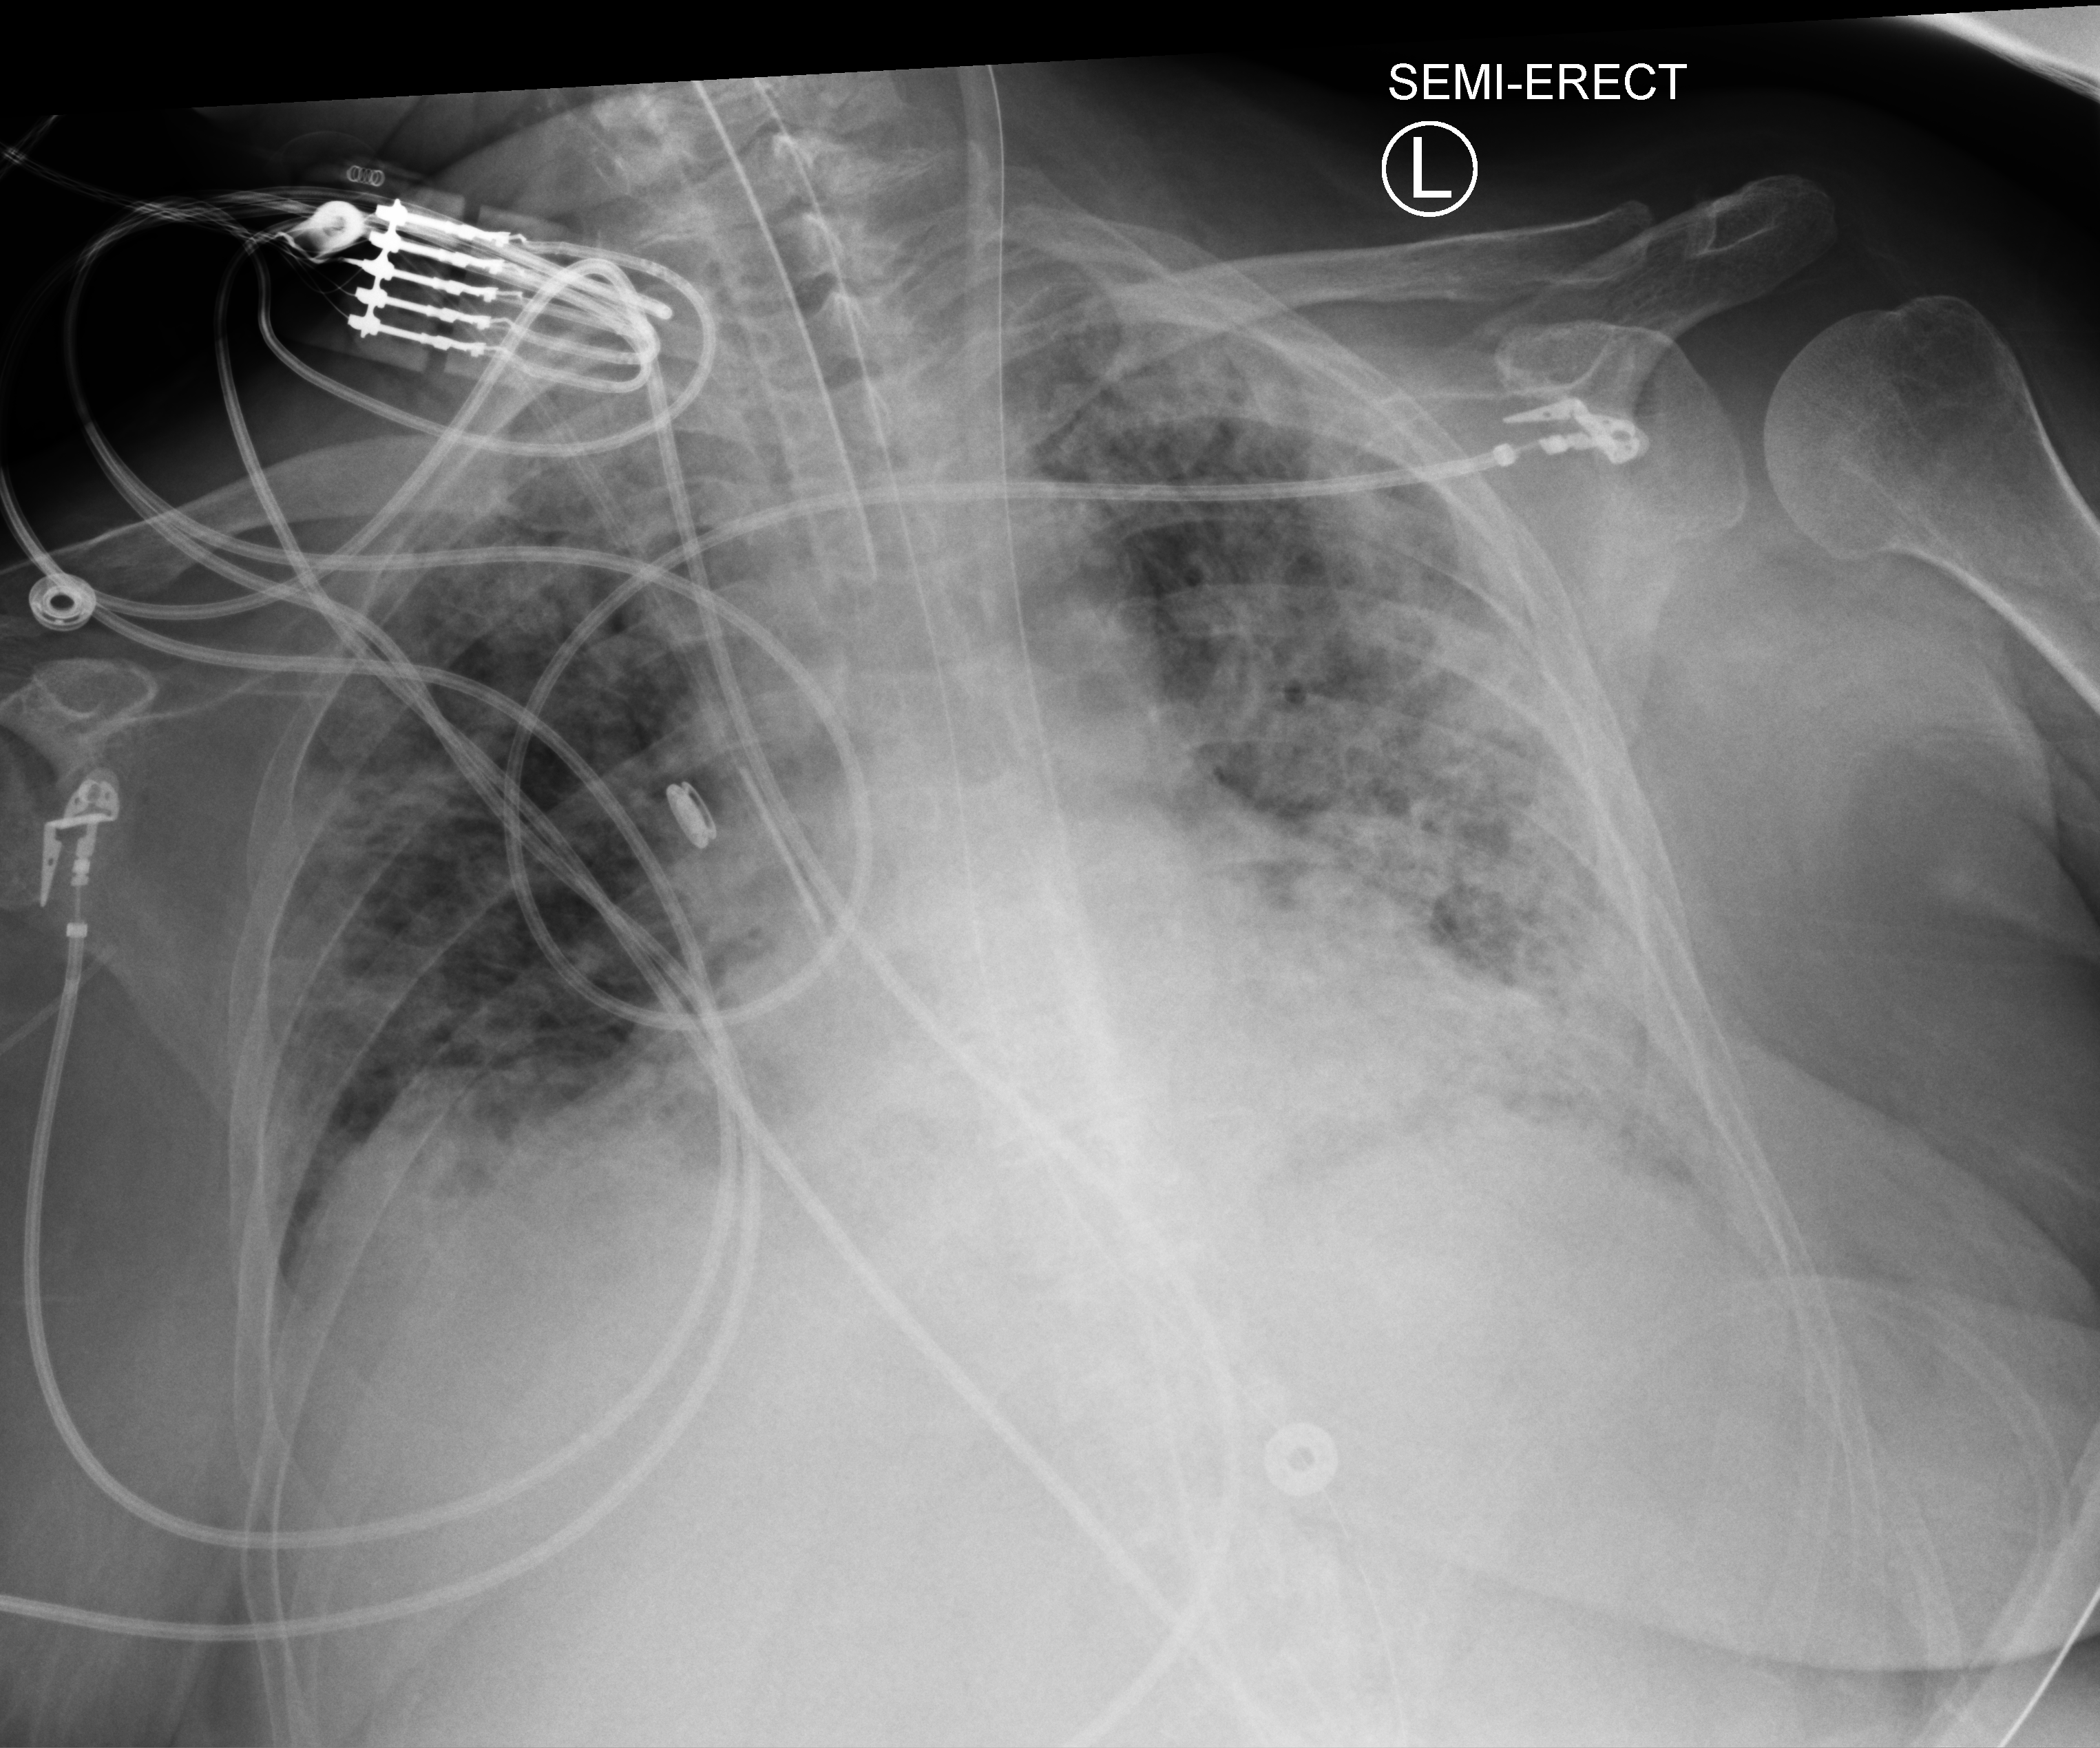
Portable chest radiograph; anteroposterior (AP) projection. Female patient hospitalised with COVID-19, age 75–90 years.
Admission-level facts for this patient (not findings on this image; timing relative to this image not recorded): hypertension (admission record): yes; mechanically ventilated during this hospital stay: yes.